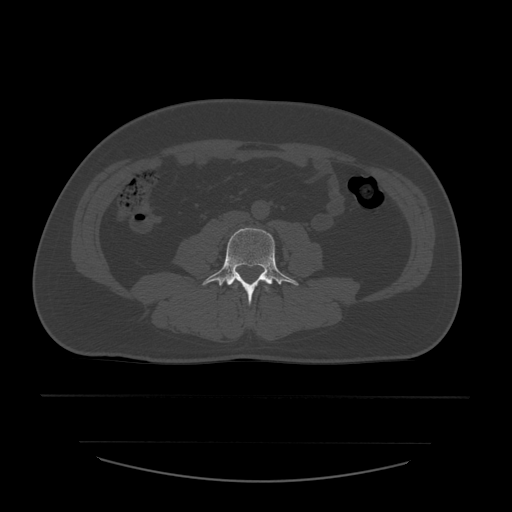
CT including the spine, one axial slice. Slice 151 of 532 in the series (ordered by position). Reconstruction kernel STANDARD. 120 kVp. Bone window (W 1800 / L 400 HU). 1.25 mm slice thickness. 512 × 512 image matrix, field of view 441 × 441 mm. Patient age 44 years. Case-level facts recorded for this patient, not image findings: primary cancer: soft tissue sarcoma.
Structures marked on this image (semi-automatic segmentation, software-assisted and operator-edited):
- L3 vertebra: bounding box [x1, y1, x2, y2] px = [233, 284, 270, 292]
- L4 vertebra: [202, 228, 299, 304]